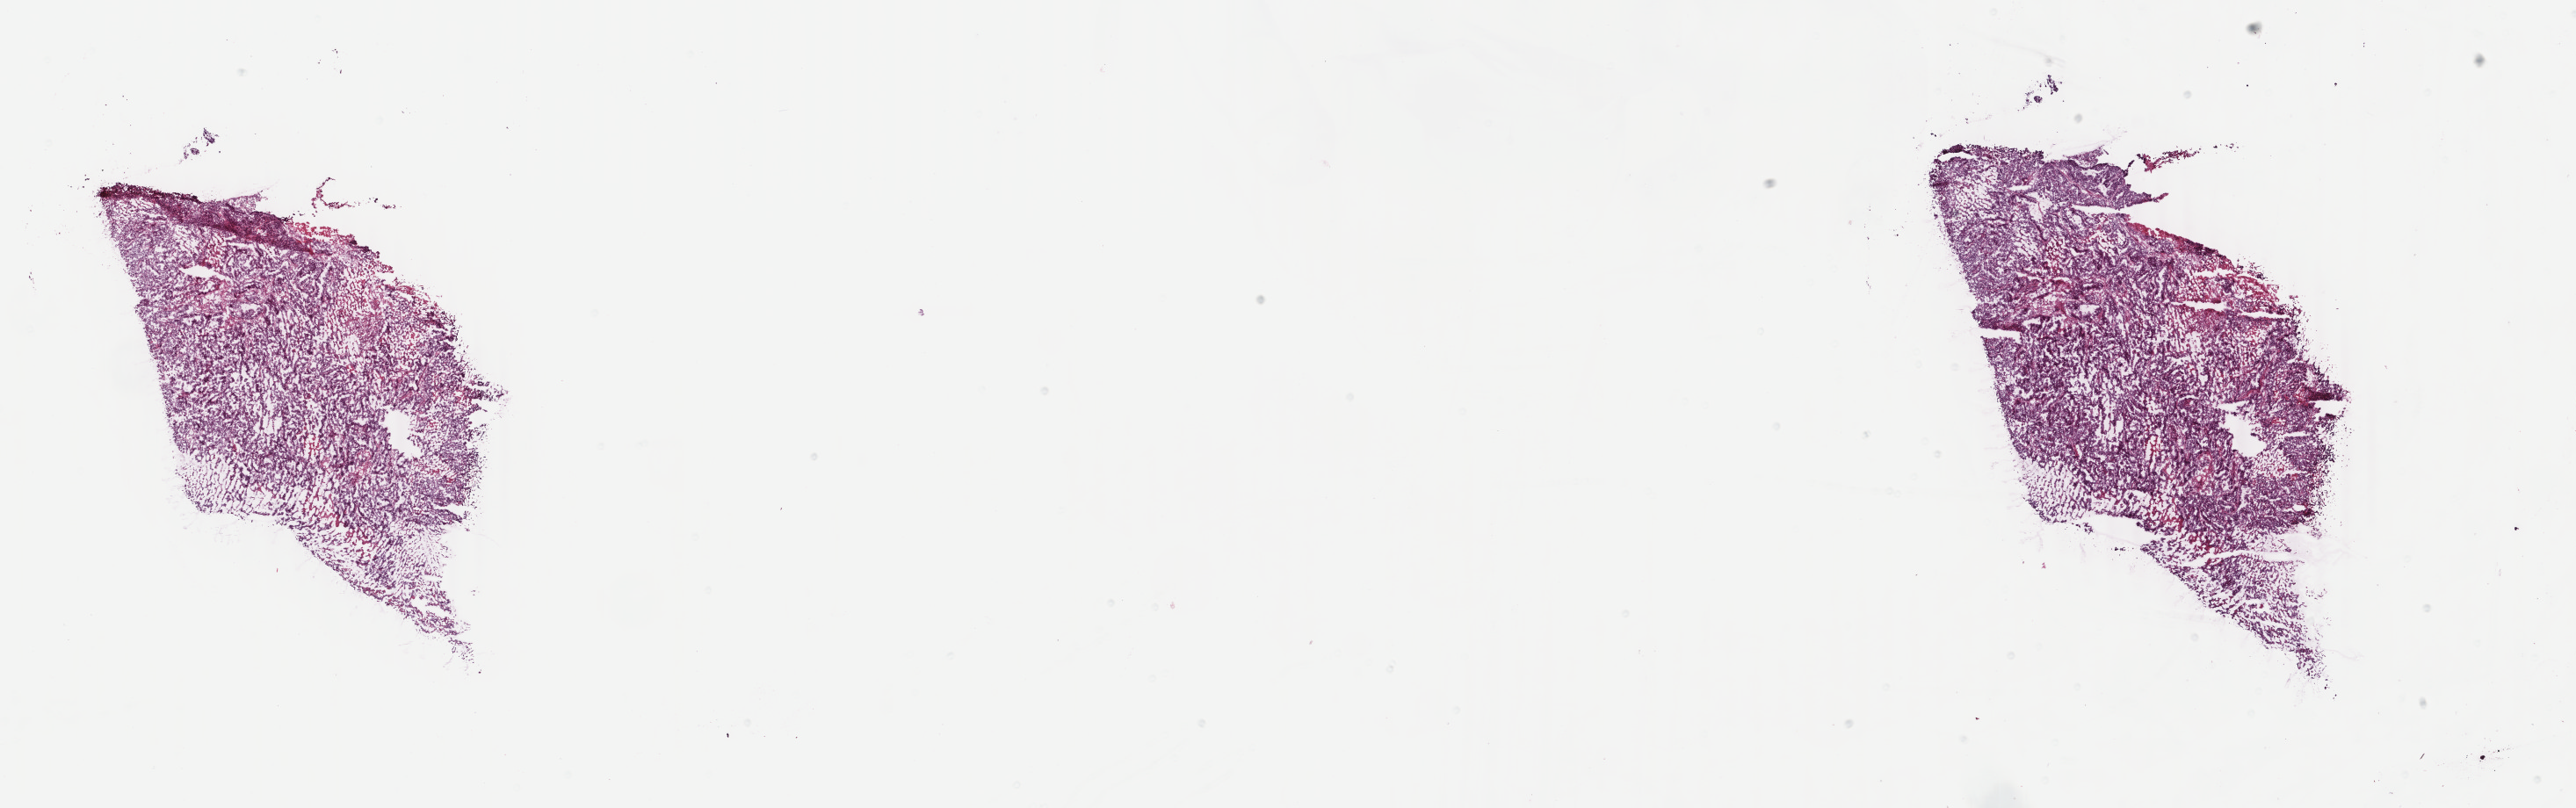
Digitized H&E-stained tissue section (whole slide) — shown as a low-resolution overview of the whole scanned area (about 23.3 x 7.3 mm, slide scanned at 40x). Frozen section from the bottom of the tissue portion. Sample: primary tumour, uterus. Female patient; age at initial diagnosis 47 years. Histologic grade: G2 (moderately differentiated). Slide review estimates, as recorded: tumour cells 75%, tumour nuclei 90%, normal cells 0%, stromal cells 5%, necrosis 20%. Inflammatory infiltration, as recorded: lymphocyte infiltration 1%, monocyte infiltration 0%, neutrophil infiltration 0%.
* lymph nodes positive (case pathology): 0 of 3 examined
* FIGO stage: IB
* diagnosis: Endometrioid adenocarcinoma, NOS